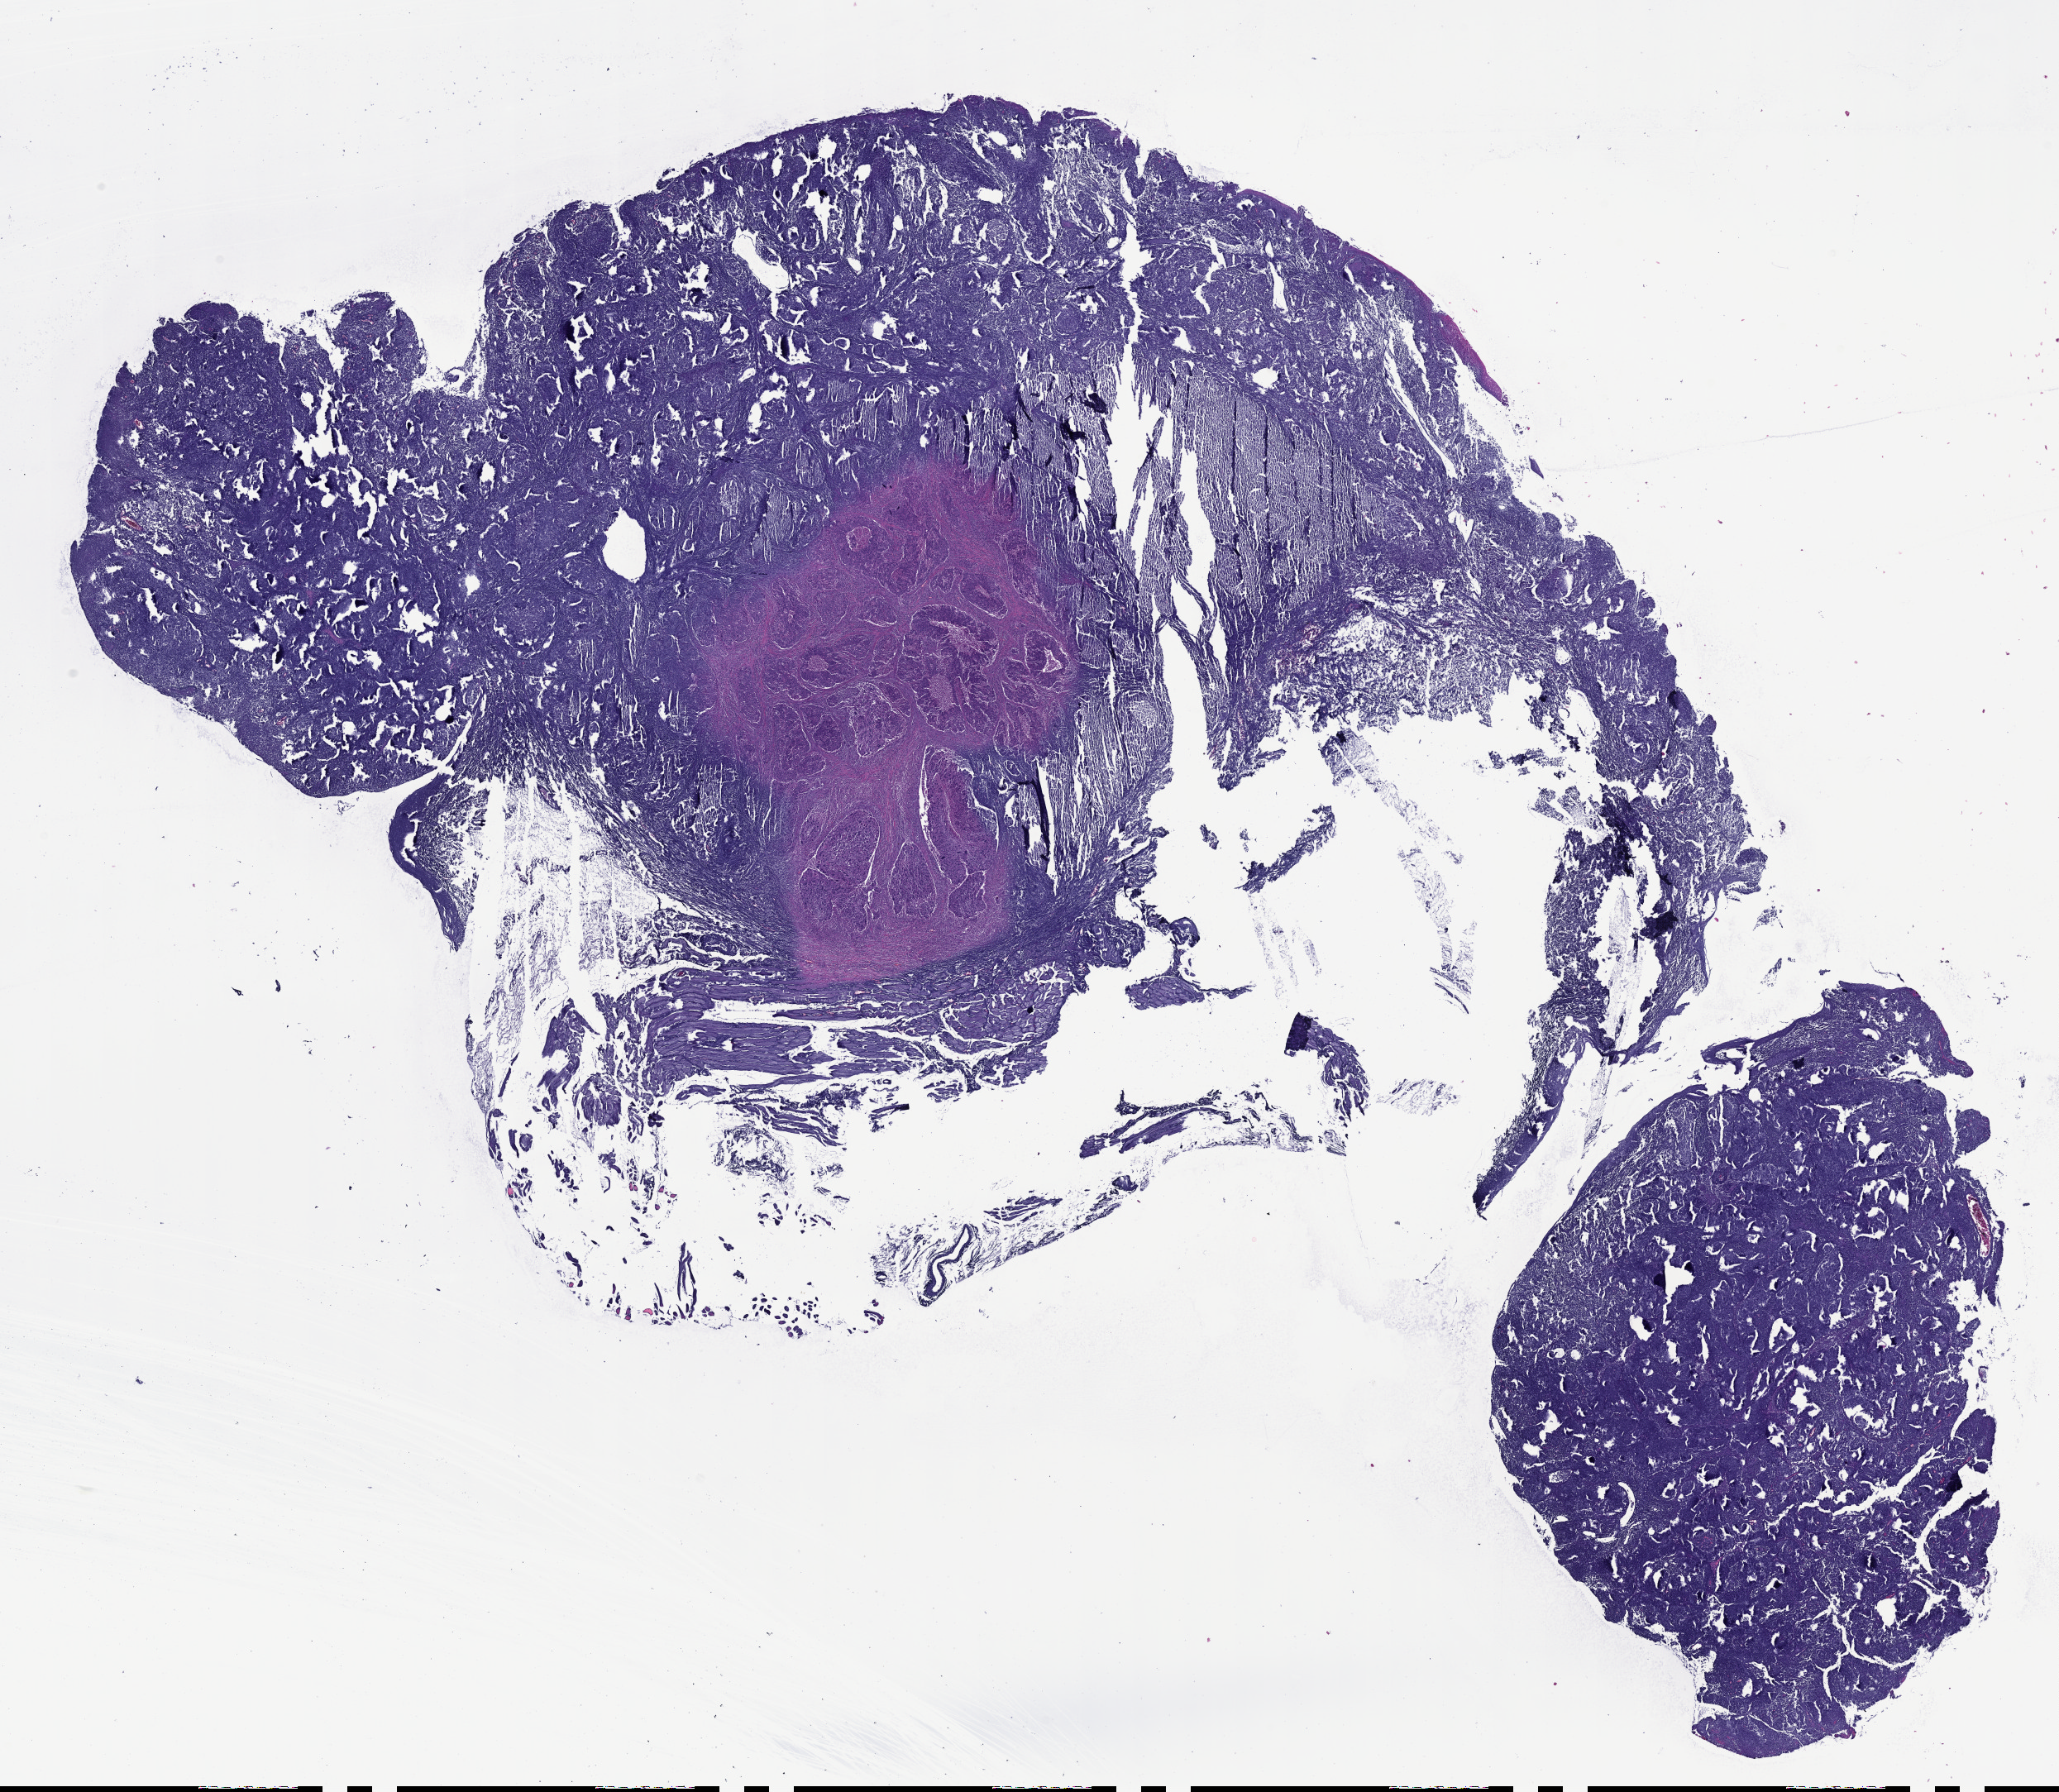
H&E-stained whole-slide image, shown as a low-resolution overview of the whole scanned area (about 20.1 x 17.5 mm); formalin-fixed paraffin-embedded (FFPE) diagnostic section; sample: primary tumour, head and neck. Male patient; age at initial diagnosis 73 years. Histologic grade: G3 (poorly differentiated).
* diagnosis: Squamous cell carcinoma, NOS (larynx, NOS)
* AJCC pathologic stage: IVA